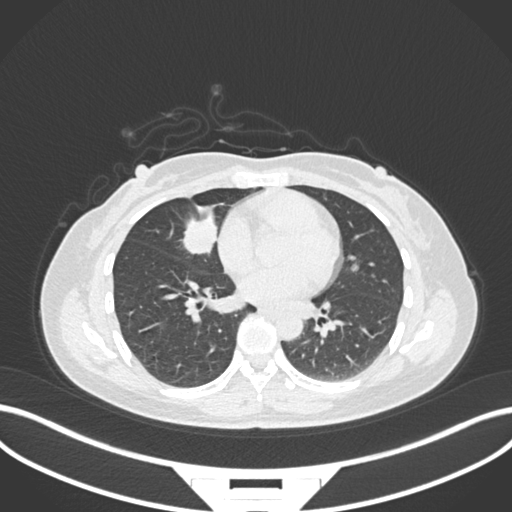
Chest CT, one axial slice; slice 72 of 171 in the series (ordered by position); lung window (W 1500 / L -600 HU); 1 mm slice thickness; 512 × 512 image matrix, field of view 400 × 400 mm. Patient: female, 43 years. From the clinical record (not read from this slice): clinical TNM (as recorded): T1c N3 M1; histopathological grade: G1.
Outlined on this slice (rectangle marked by the reading radiologist):
- lung tumour (recorded histology: adenocarcinoma): bounding box (x1, y1, x2, y2) in pixels: (176, 211, 219, 261)